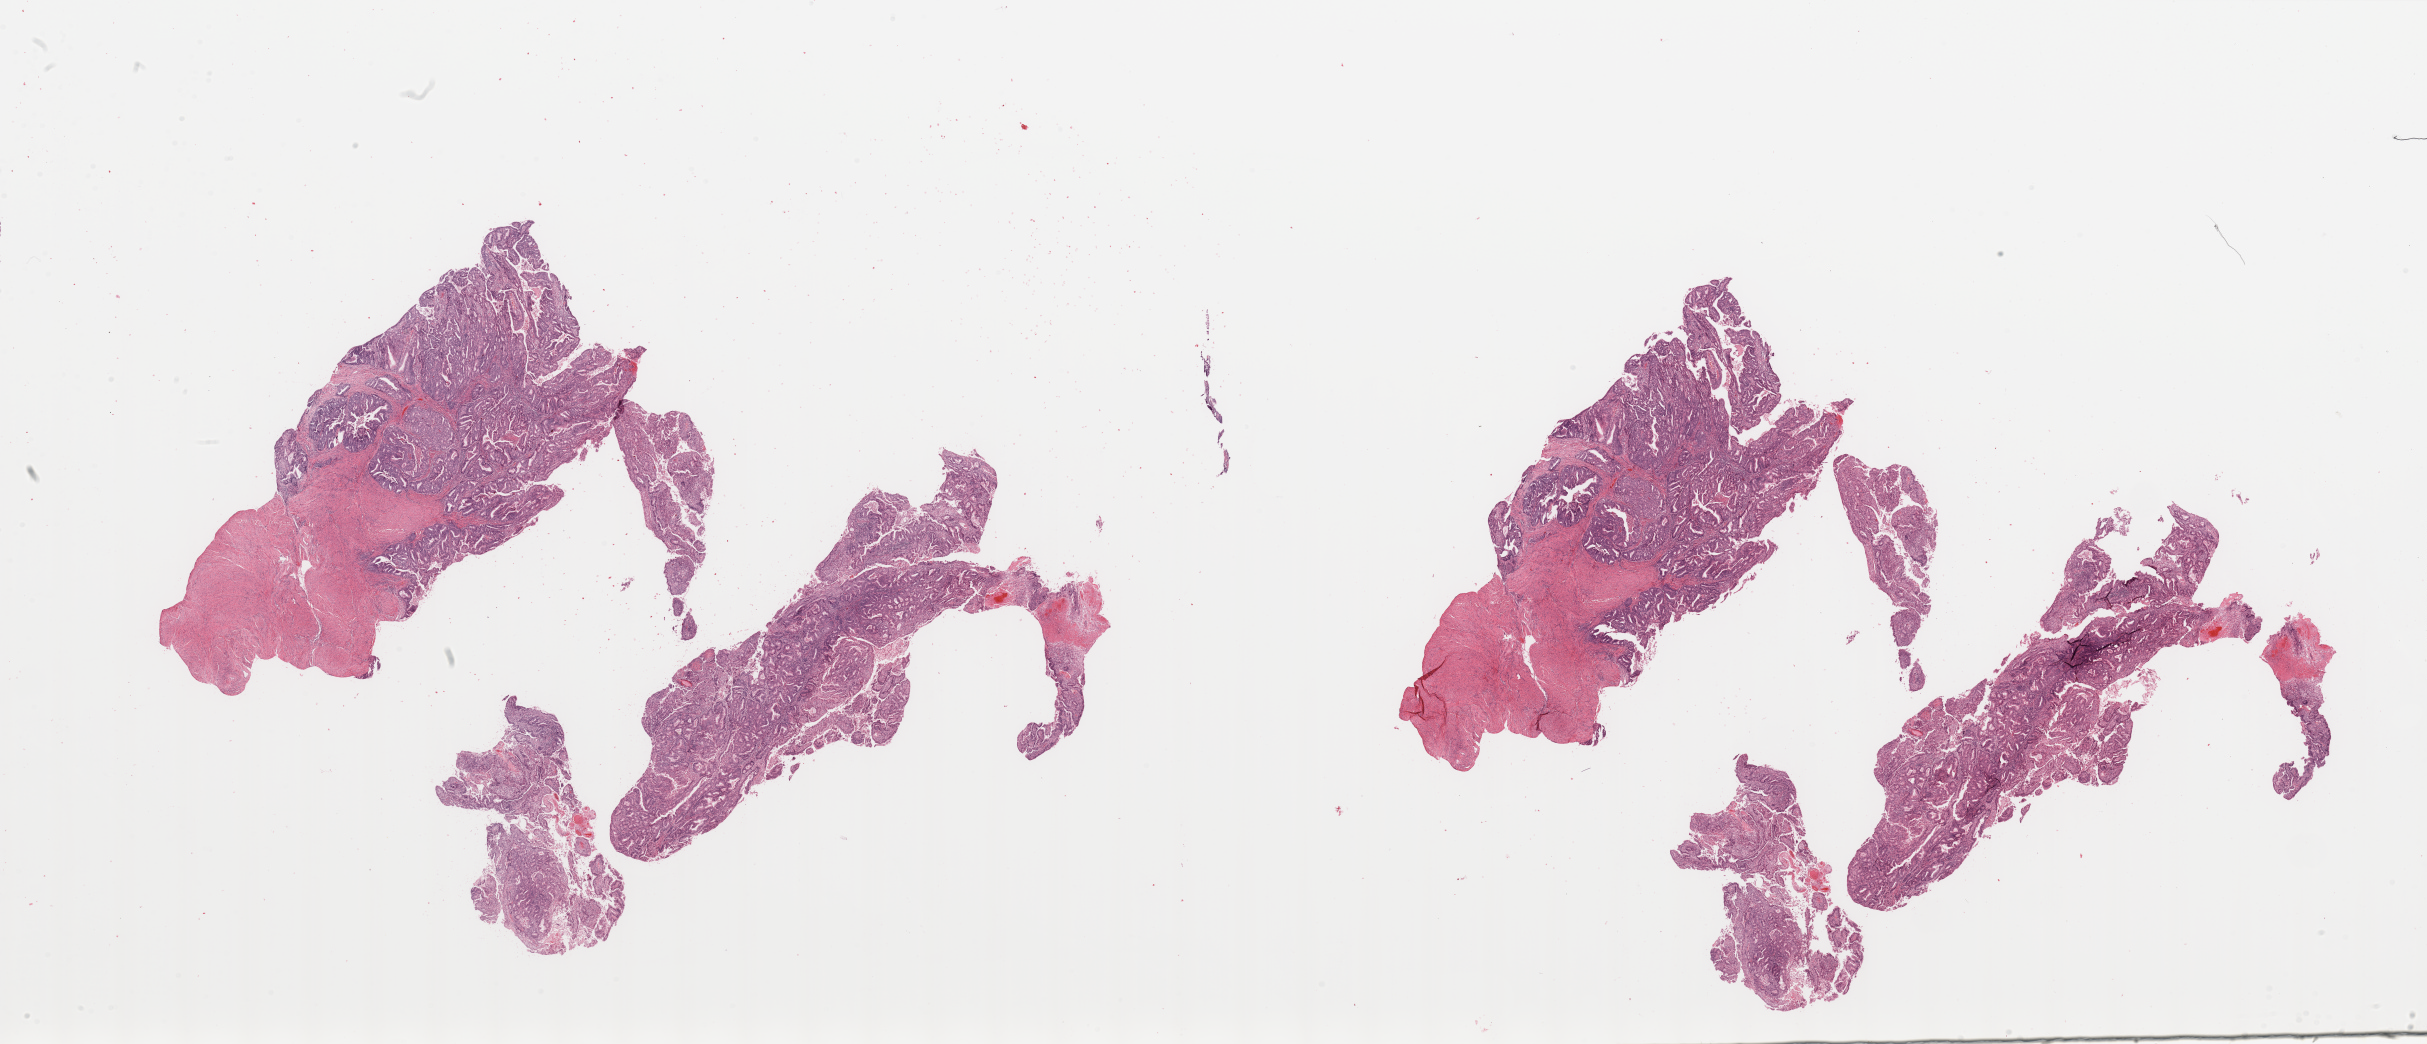
Whole-slide histology image, Hematoxylin and eosin (H&E) stained, shown as a low-resolution overview of the whole scanned area (about 38.4 x 16.5 mm). Tumour tissue sample, uterus. 51-year-old female patient. Histologic grade: G1 (well differentiated).
Histologic diagnosis: Endometrioid adenocarcinoma, NOS. AJCC pathologic stage: I.